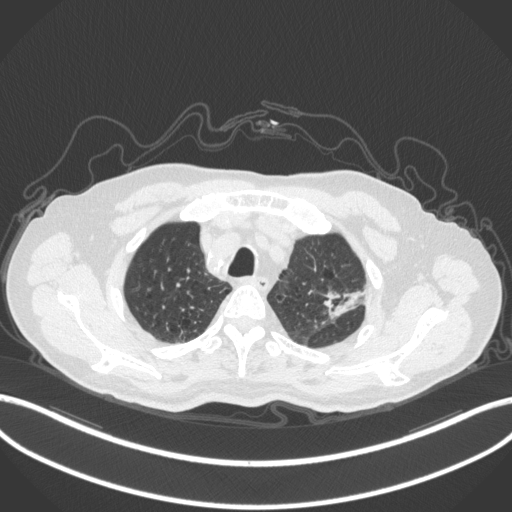
Chest CT, one axial slice. Position 253 of 331 along the scan axis. Reconstruction kernel B31f. 120 kVp. Lung window (W 1500 / L -600 HU). 512 × 512 image matrix, field of view 400 × 400 mm. Patient: male, 79 years. From the clinical record (not read from this slice): clinical TNM (as recorded): T2a N1 M1.
Outlined on this slice (rectangle marked by the reading radiologist):
- lung tumour (recorded histology: adenocarcinoma): bounding box [x1, y1, x2, y2] px = [325, 287, 368, 321]